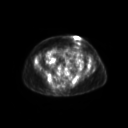
FDG PET of an extremity soft-tissue mass (from a PET/CT study), one axial slice. 128 × 128 image matrix, field of view 600 × 600 mm. Female patient, age 60 years. From the clinical record (not read from this slice): histological type: spindle cell suggestive of myxofibrosarcoma; grade: intermediate; site of the primary tumour: right buttock.
Annotated regions visible in this slice (expert contour drawn on MRI and transferred to this co-registered scan by the dataset authors):
- gross tumour volume (mass): bounding box <49,83,61,90> (left, top, right, bottom; pixels)